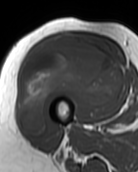
MRI of an extremity soft-tissue mass, one axial slice; position 47 of 99 along the scan axis; MR volume resampled by the dataset authors to the PET/CT grid (not the native acquisition matrix); 138 × 172 image matrix, field of view 135 × 168 mm. Female patient. From the clinical record (not read from this slice): histological type: pleiomorphic undifferentiated sarcoma; grade: high; site of the primary tumour: right quadricep.
Annotated regions visible in this slice (expert contour drawn on MRI and transferred to this co-registered scan by the dataset authors):
- gross tumour volume including surrounding oedema: bounding box [x1, y1, x2, y2] px = [19, 34, 122, 135]
- gross tumour volume (mass): [19, 34, 122, 135]